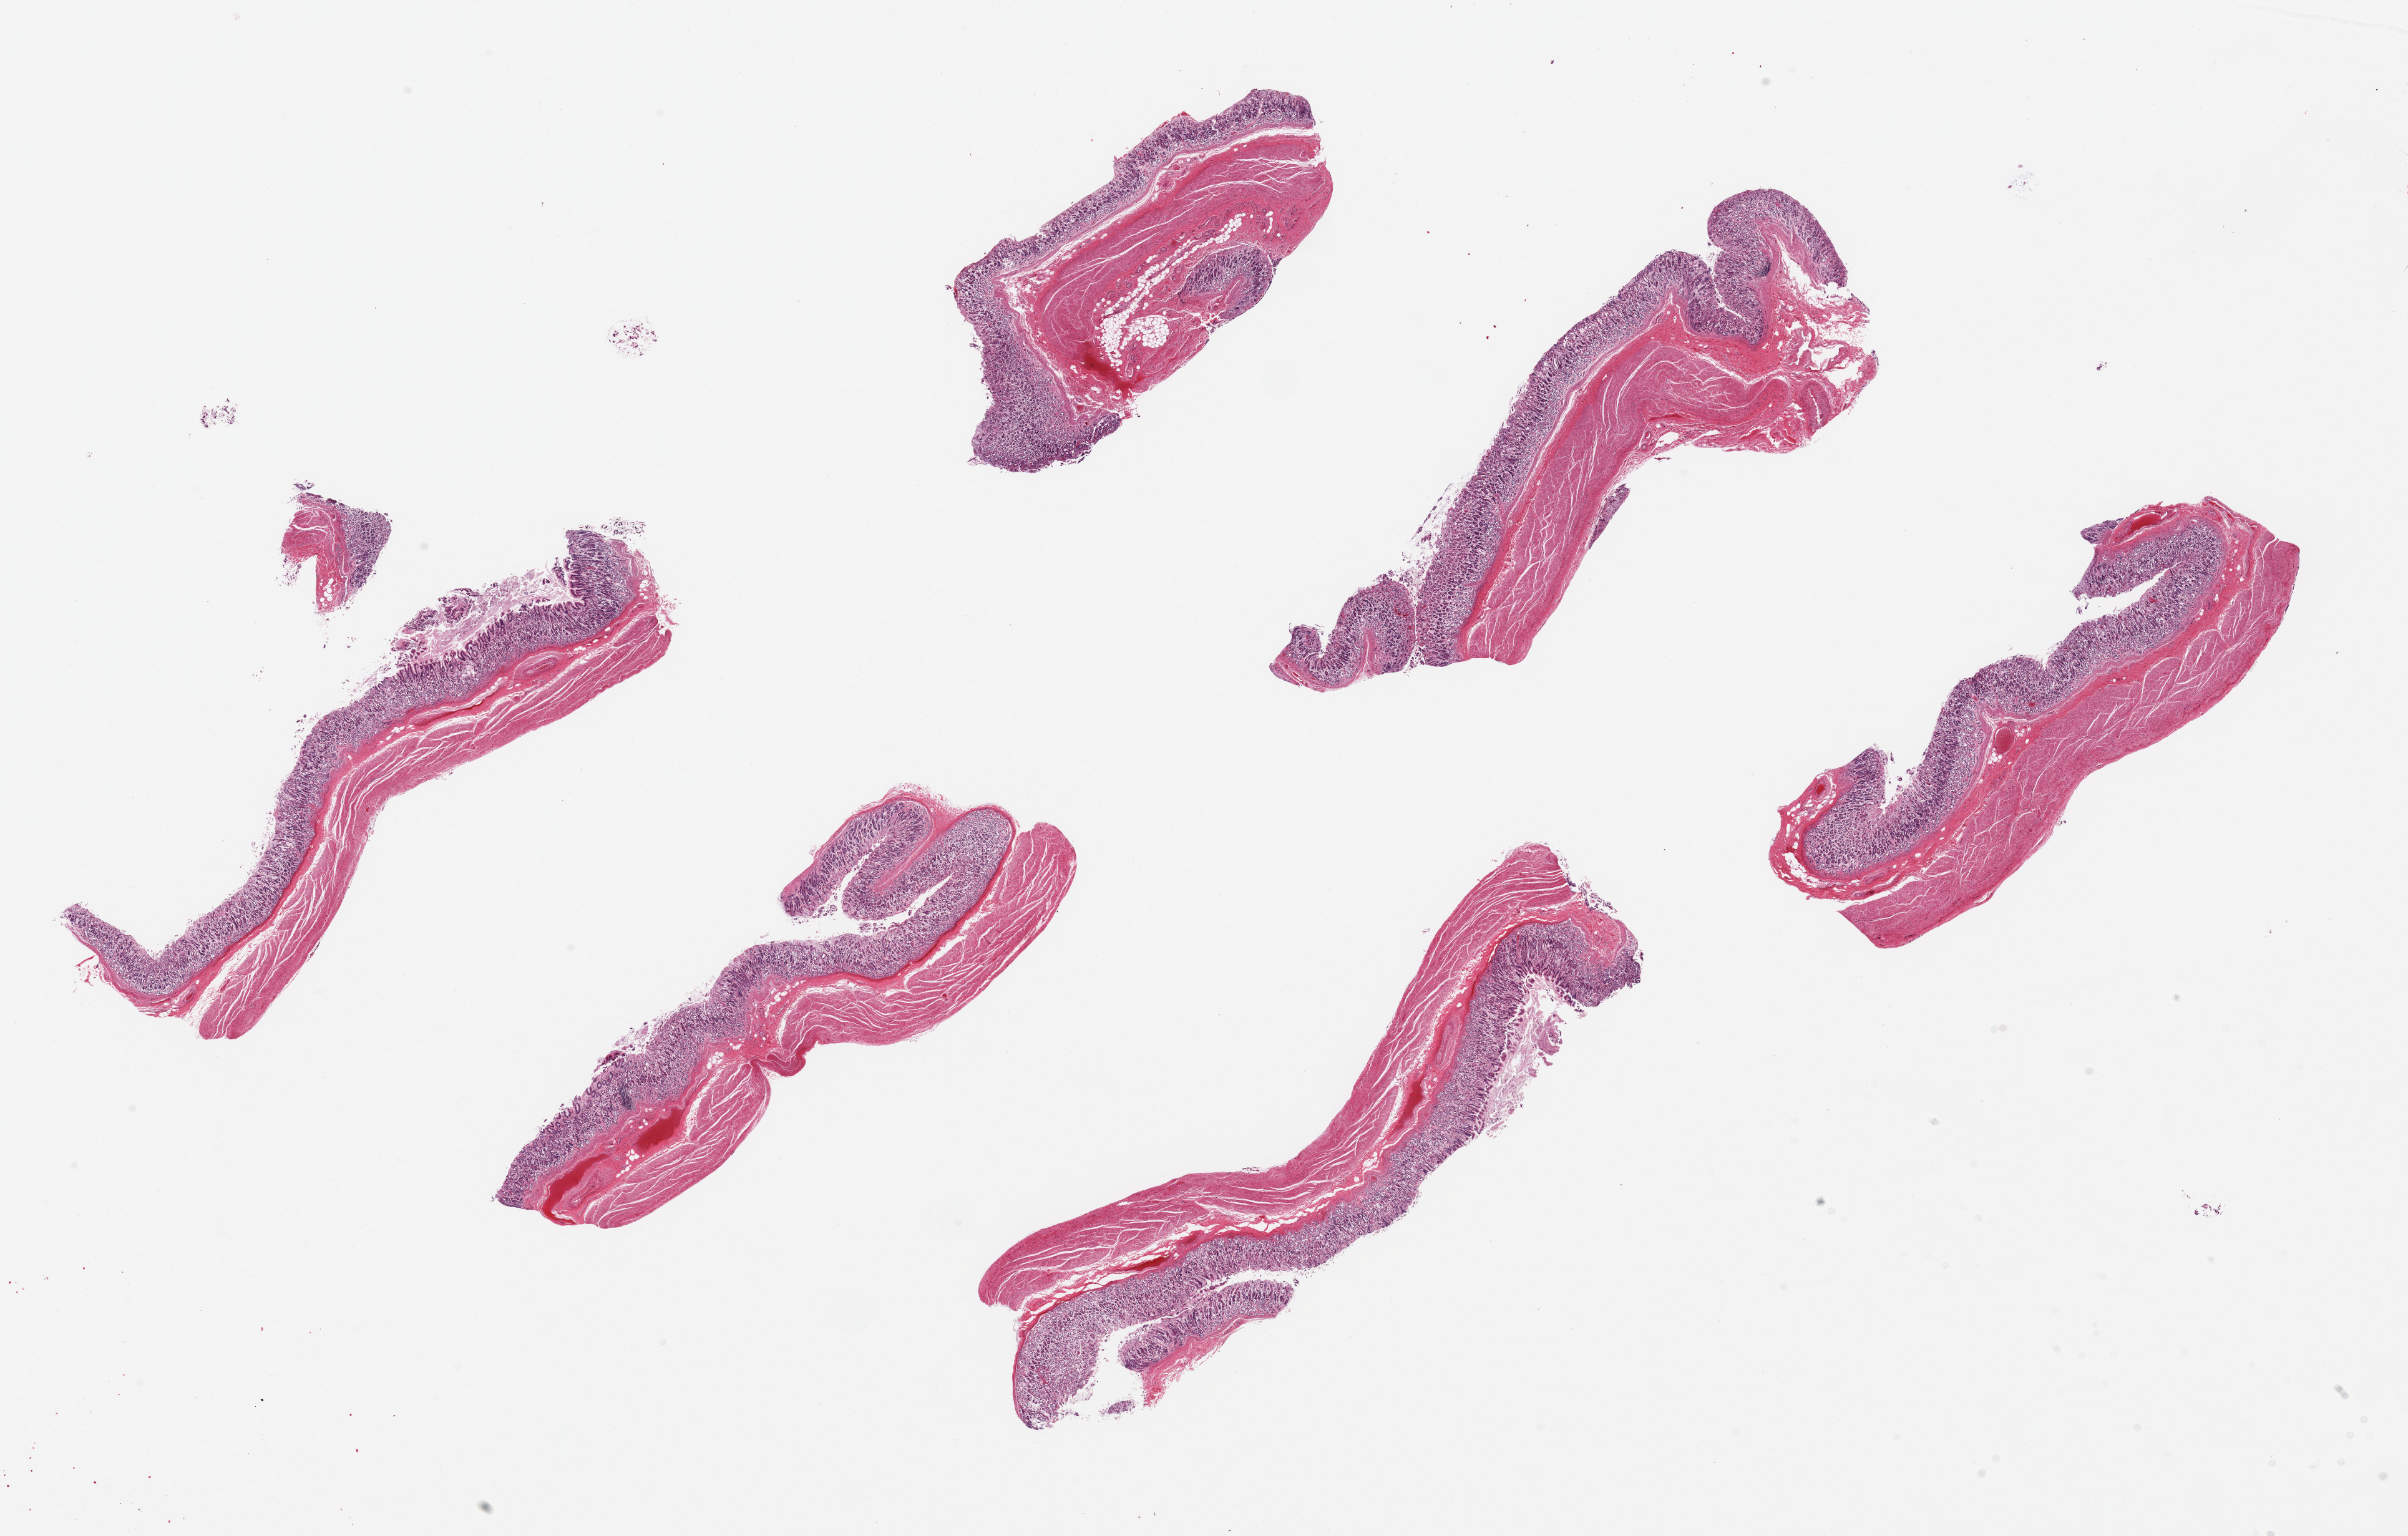
Hematoxylin and eosin (H&E) whole-slide image, brightfield — whole scanned area (about 30.5 x 19.5 mm) shown as a low-resolution overview; PAXgene-fixed, paraffin-embedded tissue; section of stomach (target tissue); tissue donor sample.
Review note (as recorded): 6 pieces up to 10x3 mm; mucosa moderately autolyzed, muscularis mildly autolyzed.